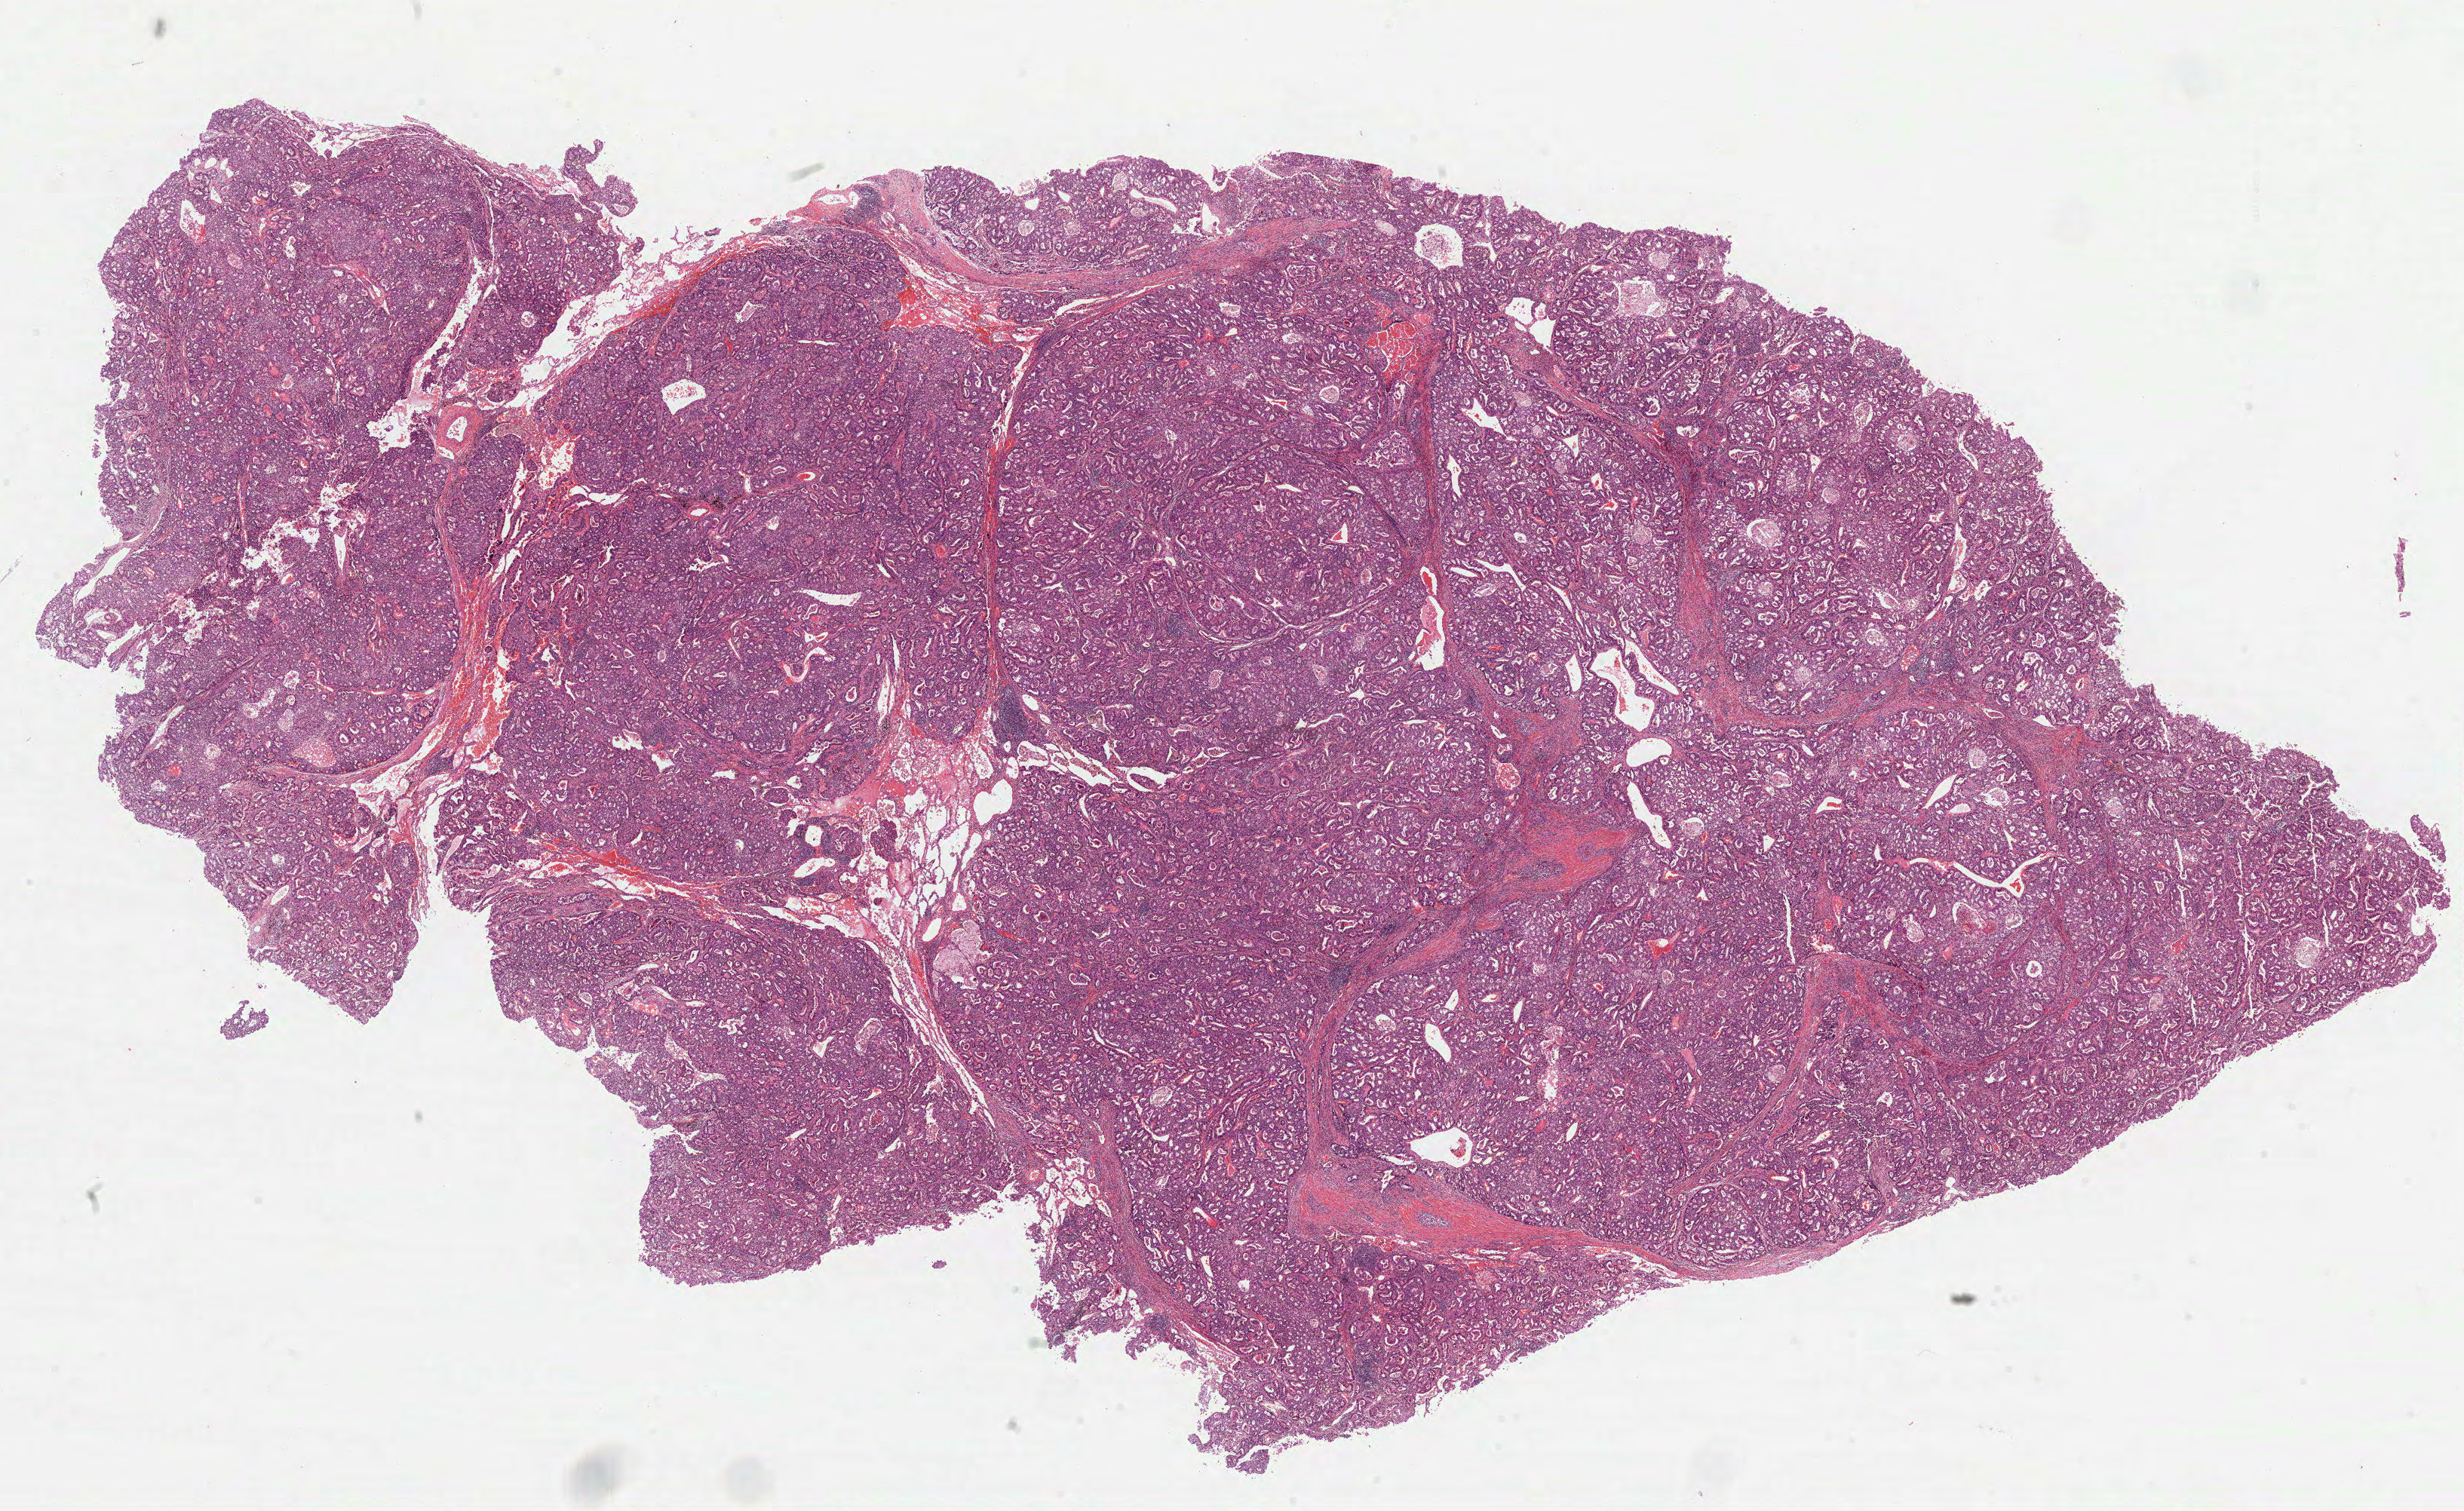
Digitized H&E-stained tissue section (whole slide) — shown as a low-resolution overview of the whole scanned area (about 26.3 x 16.2 mm). Formalin-fixed paraffin-embedded (FFPE) diagnostic section. Sample: primary tumour, lung. Patient: male, age at initial diagnosis 64 years.
AJCC pathologic stage: IA (7th edition). Diagnosis: Adenocarcinoma, NOS (upper lobe, lung). Laterality: right.